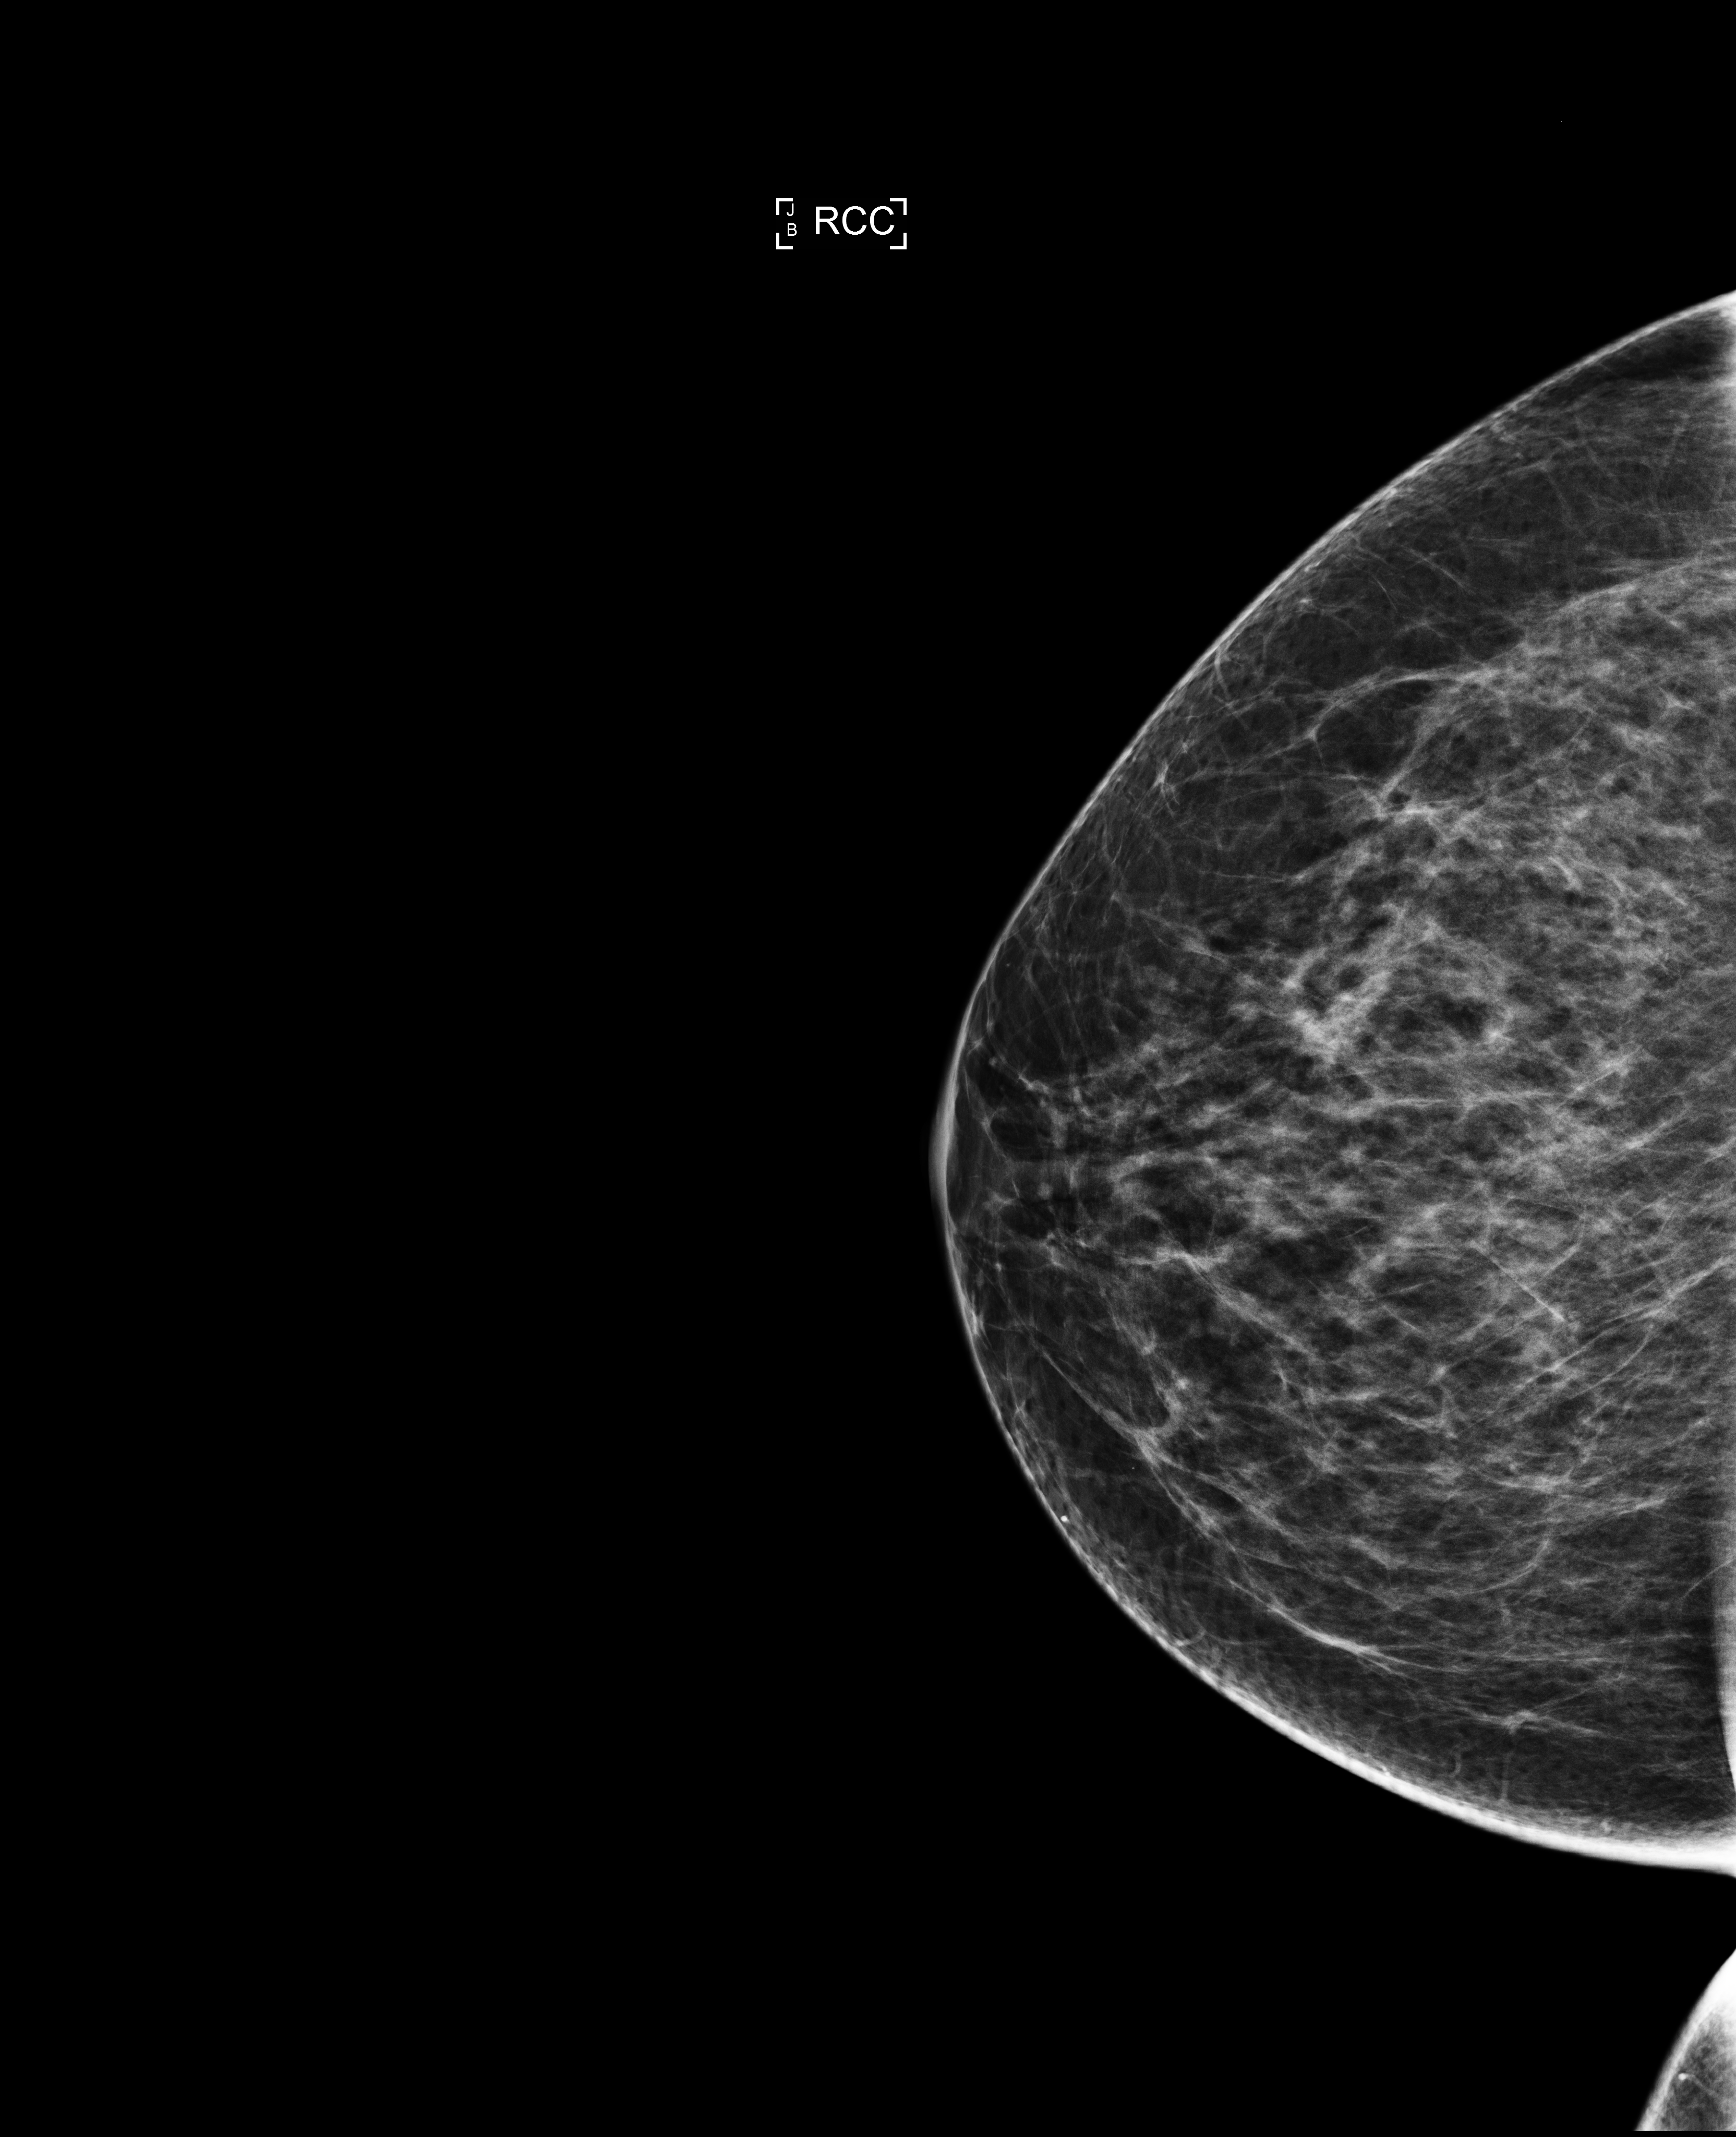
Digital mammogram (FFDM); right breast; cranio-caudal projection; annual screening mammography examination; system: Selenia Dimensions. Patient aged 62 years (female).
Breast density at the screening exam (both breasts): scattered fibroglandular densities (BI-RADS density category b). Final BI-RADS assessment for this screening round (tomosynthesis exam, both breasts): category 2. Recall: recalled for additional imaging after this screen.